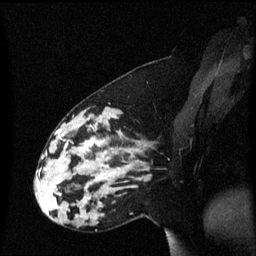
Breast MRI (dynamic contrast-enhanced), one sagittal slice. Position 20 of 60 along the scan axis. Dynamic contrast-enhanced series, image 2 of 3 at this slice position (ordered by acquisition). 1.5 T. TE 4.2 ms, TR 8.4 ms. 2 mm slice thickness. 256 × 256 image matrix, field of view 210 × 210 mm. Female patient, age 33 years. Case-level facts recorded for this patient, not image findings: setting: breast cancer imaged before/during neoadjuvant chemotherapy; receptor status: triple-negative.
Structures marked on this image (semi-automatically segmented with operator editing):
- analysis volume of interest (the breast-tissue region the enhancement analysis was run in; not a lesion): bounding box <44,123,139,189> (left, top, right, bottom; pixels)
- tumour enhancement mask (voxels above the 70 % enhancement threshold inside the analysis volume of interest): <48,145,101,170>